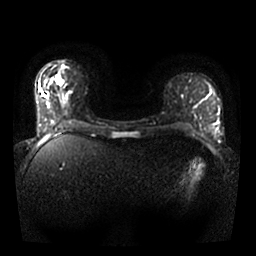
Breast MRI, one axial slice. Slice 9 of 25 in the series (ordered by position). Diffusion-weighted series; image 2 of 4 stored at this slice position (different b-values; order by instance number). 1.5 T. 4 mm slice thickness. 256 × 256 image matrix. Female patient.
Annotated regions visible in this slice (outlined manually by an expert reader):
- tumour on diffusion-weighted imaging: bounding box (x1, y1, x2, y2) in pixels: (44, 78, 63, 85)